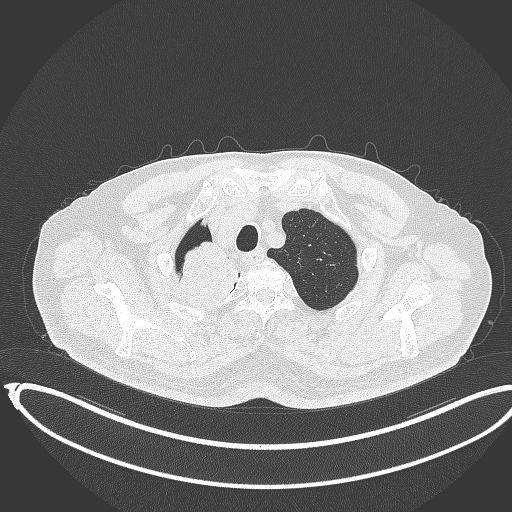
Chest CT, one axial slice. Slice 324 of 403 in the series (ordered by position). Reconstruction kernel B70f. Lung window (W 1500 / L -600 HU). 1 mm slice thickness. 512 × 512 image matrix, field of view 436 × 436 mm. Patient: male, 68 years. Case-level facts recorded for this patient, not image findings: clinical TNM (as recorded): T2a N0 M0.
Structures marked on this image (bounding box drawn by a radiologist):
- lung tumour (recorded histology: adenocarcinoma): bounding box (x1, y1, x2, y2) in pixels: (167, 238, 249, 324)